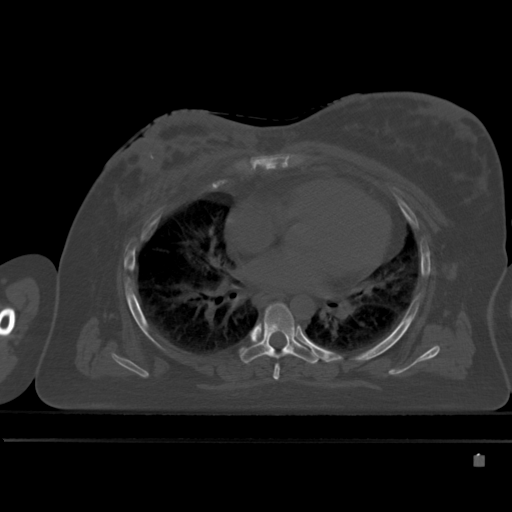
CT including the spine, one axial slice; slice 309 of 495 in the series (ordered by position); bone window (W 1800 / L 400 HU); 512 × 512 image matrix, field of view 404 × 404 mm. Female patient, age 33 years. From the clinical record (not read from this slice): primary cancer: breast.
Outlined on this slice (semi-automatic segmentation, software-assisted and operator-edited):
- T5 vertebra: bounding box (x1, y1, x2, y2) in pixels: (273, 364, 280, 380)
- T6 vertebra: (241, 303, 322, 364)